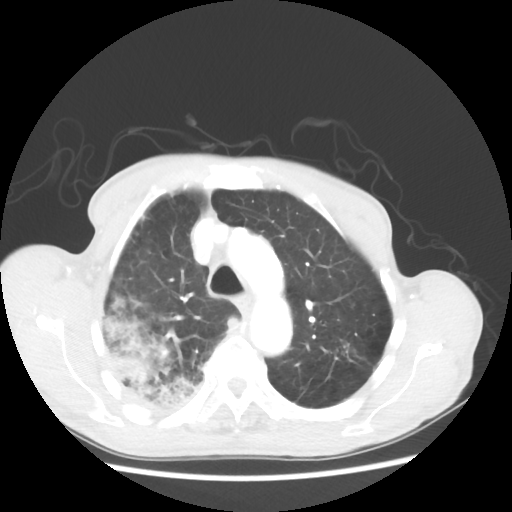
Chest CT, one axial slice; position 41 of 58 along the scan axis; reconstruction kernel STANDARD; 100 kVp; lung window (W 1500 / L -600 HU); 512 × 512 image matrix, field of view 351 × 351 mm. Male patient, age 75 years. From the clinical record (not read from this slice): clinical TNM (as recorded): T4 N1 M1.
Outlined on this slice (rectangle marked by the reading radiologist):
- lung tumour (recorded histology: adenocarcinoma): bounding box [x1, y1, x2, y2] px = [92, 289, 205, 406]